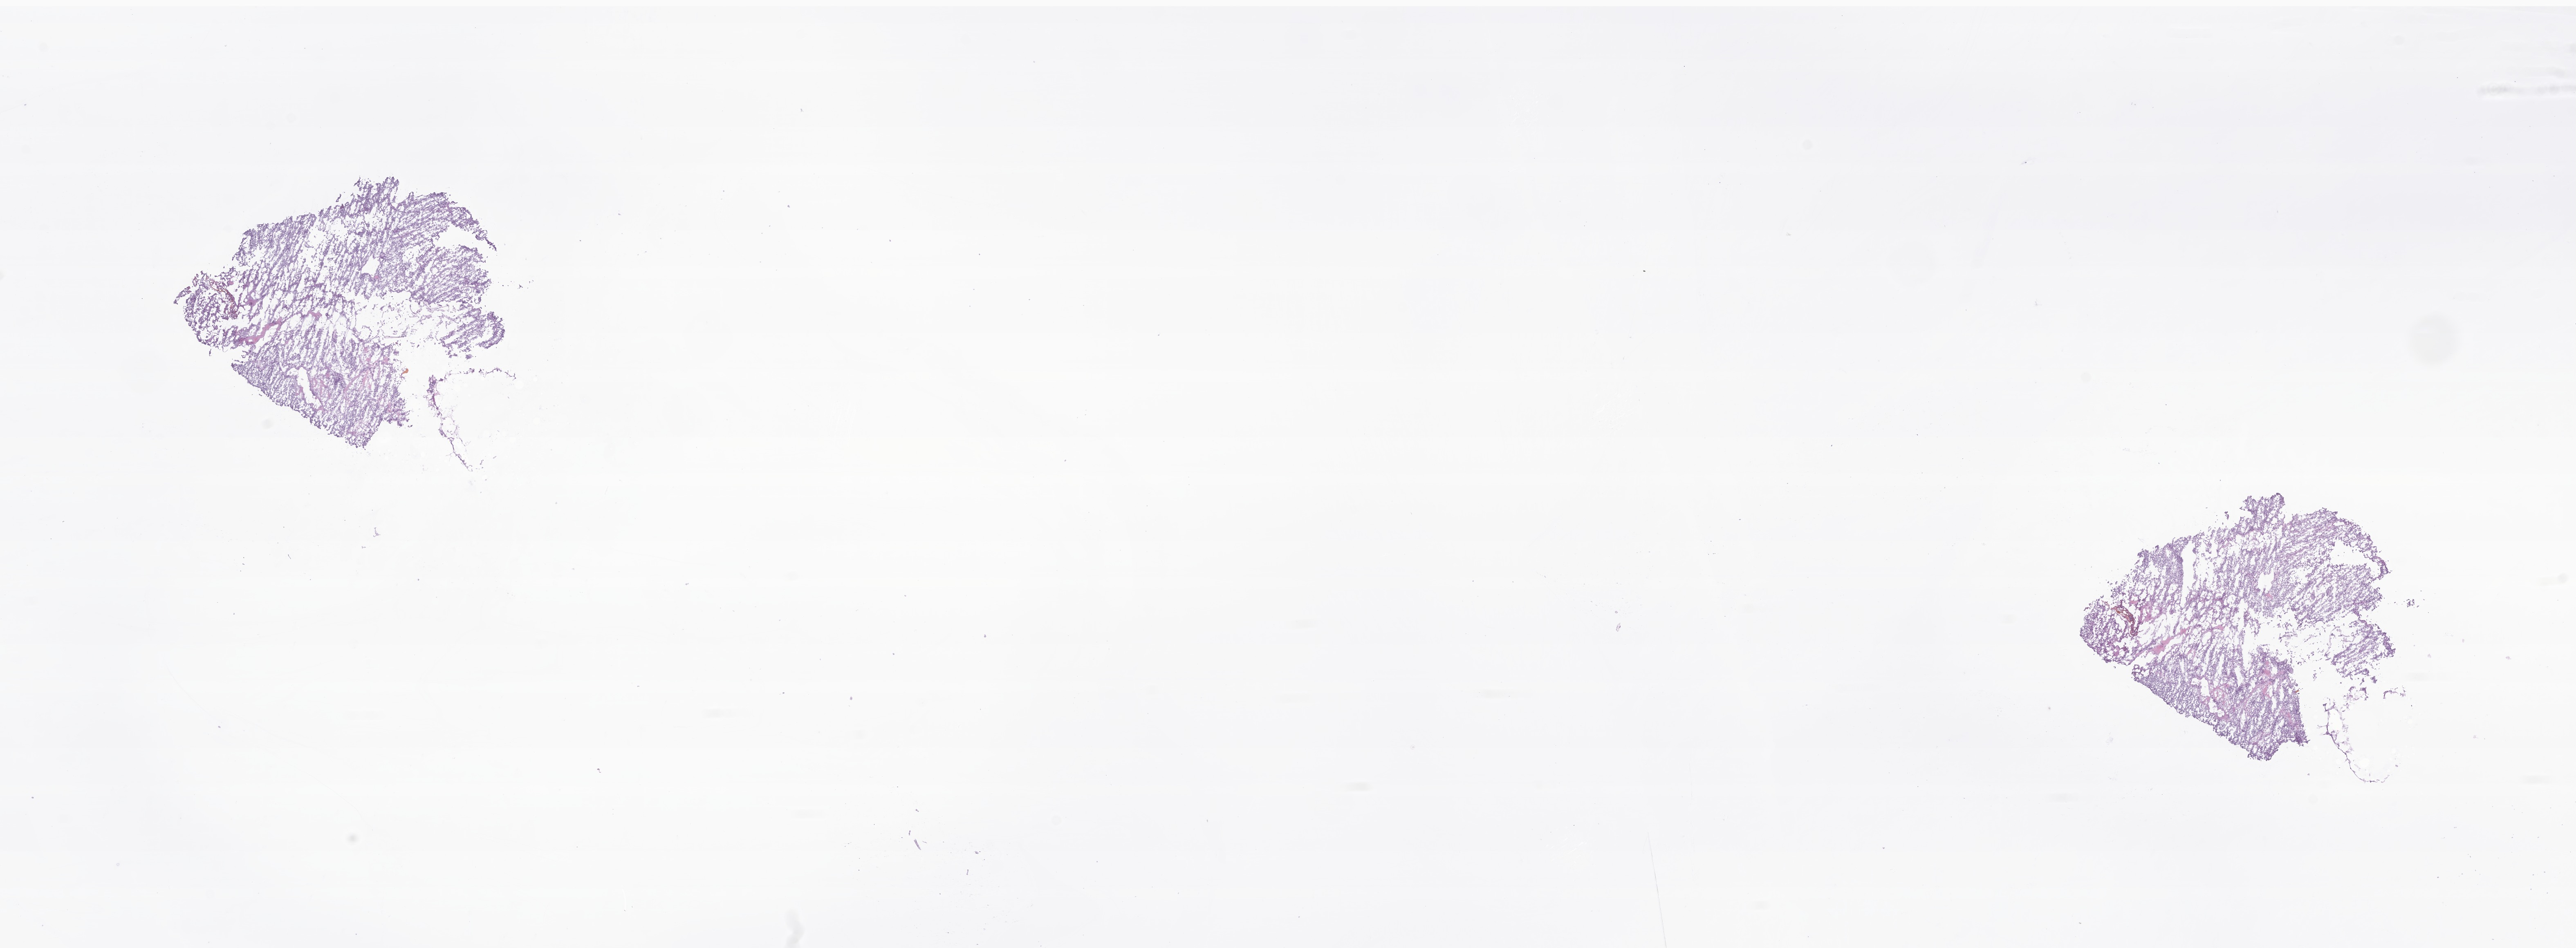
H&E whole-slide image of tumor tissue from the lower limb — low-resolution overview of the scanned area, about 26.6 x 9.8 mm, frozen section (OCT-embedded). Patient: female, age 161 months (13 years 5 months).
Diagnosis: Undifferentiated sarcoma.